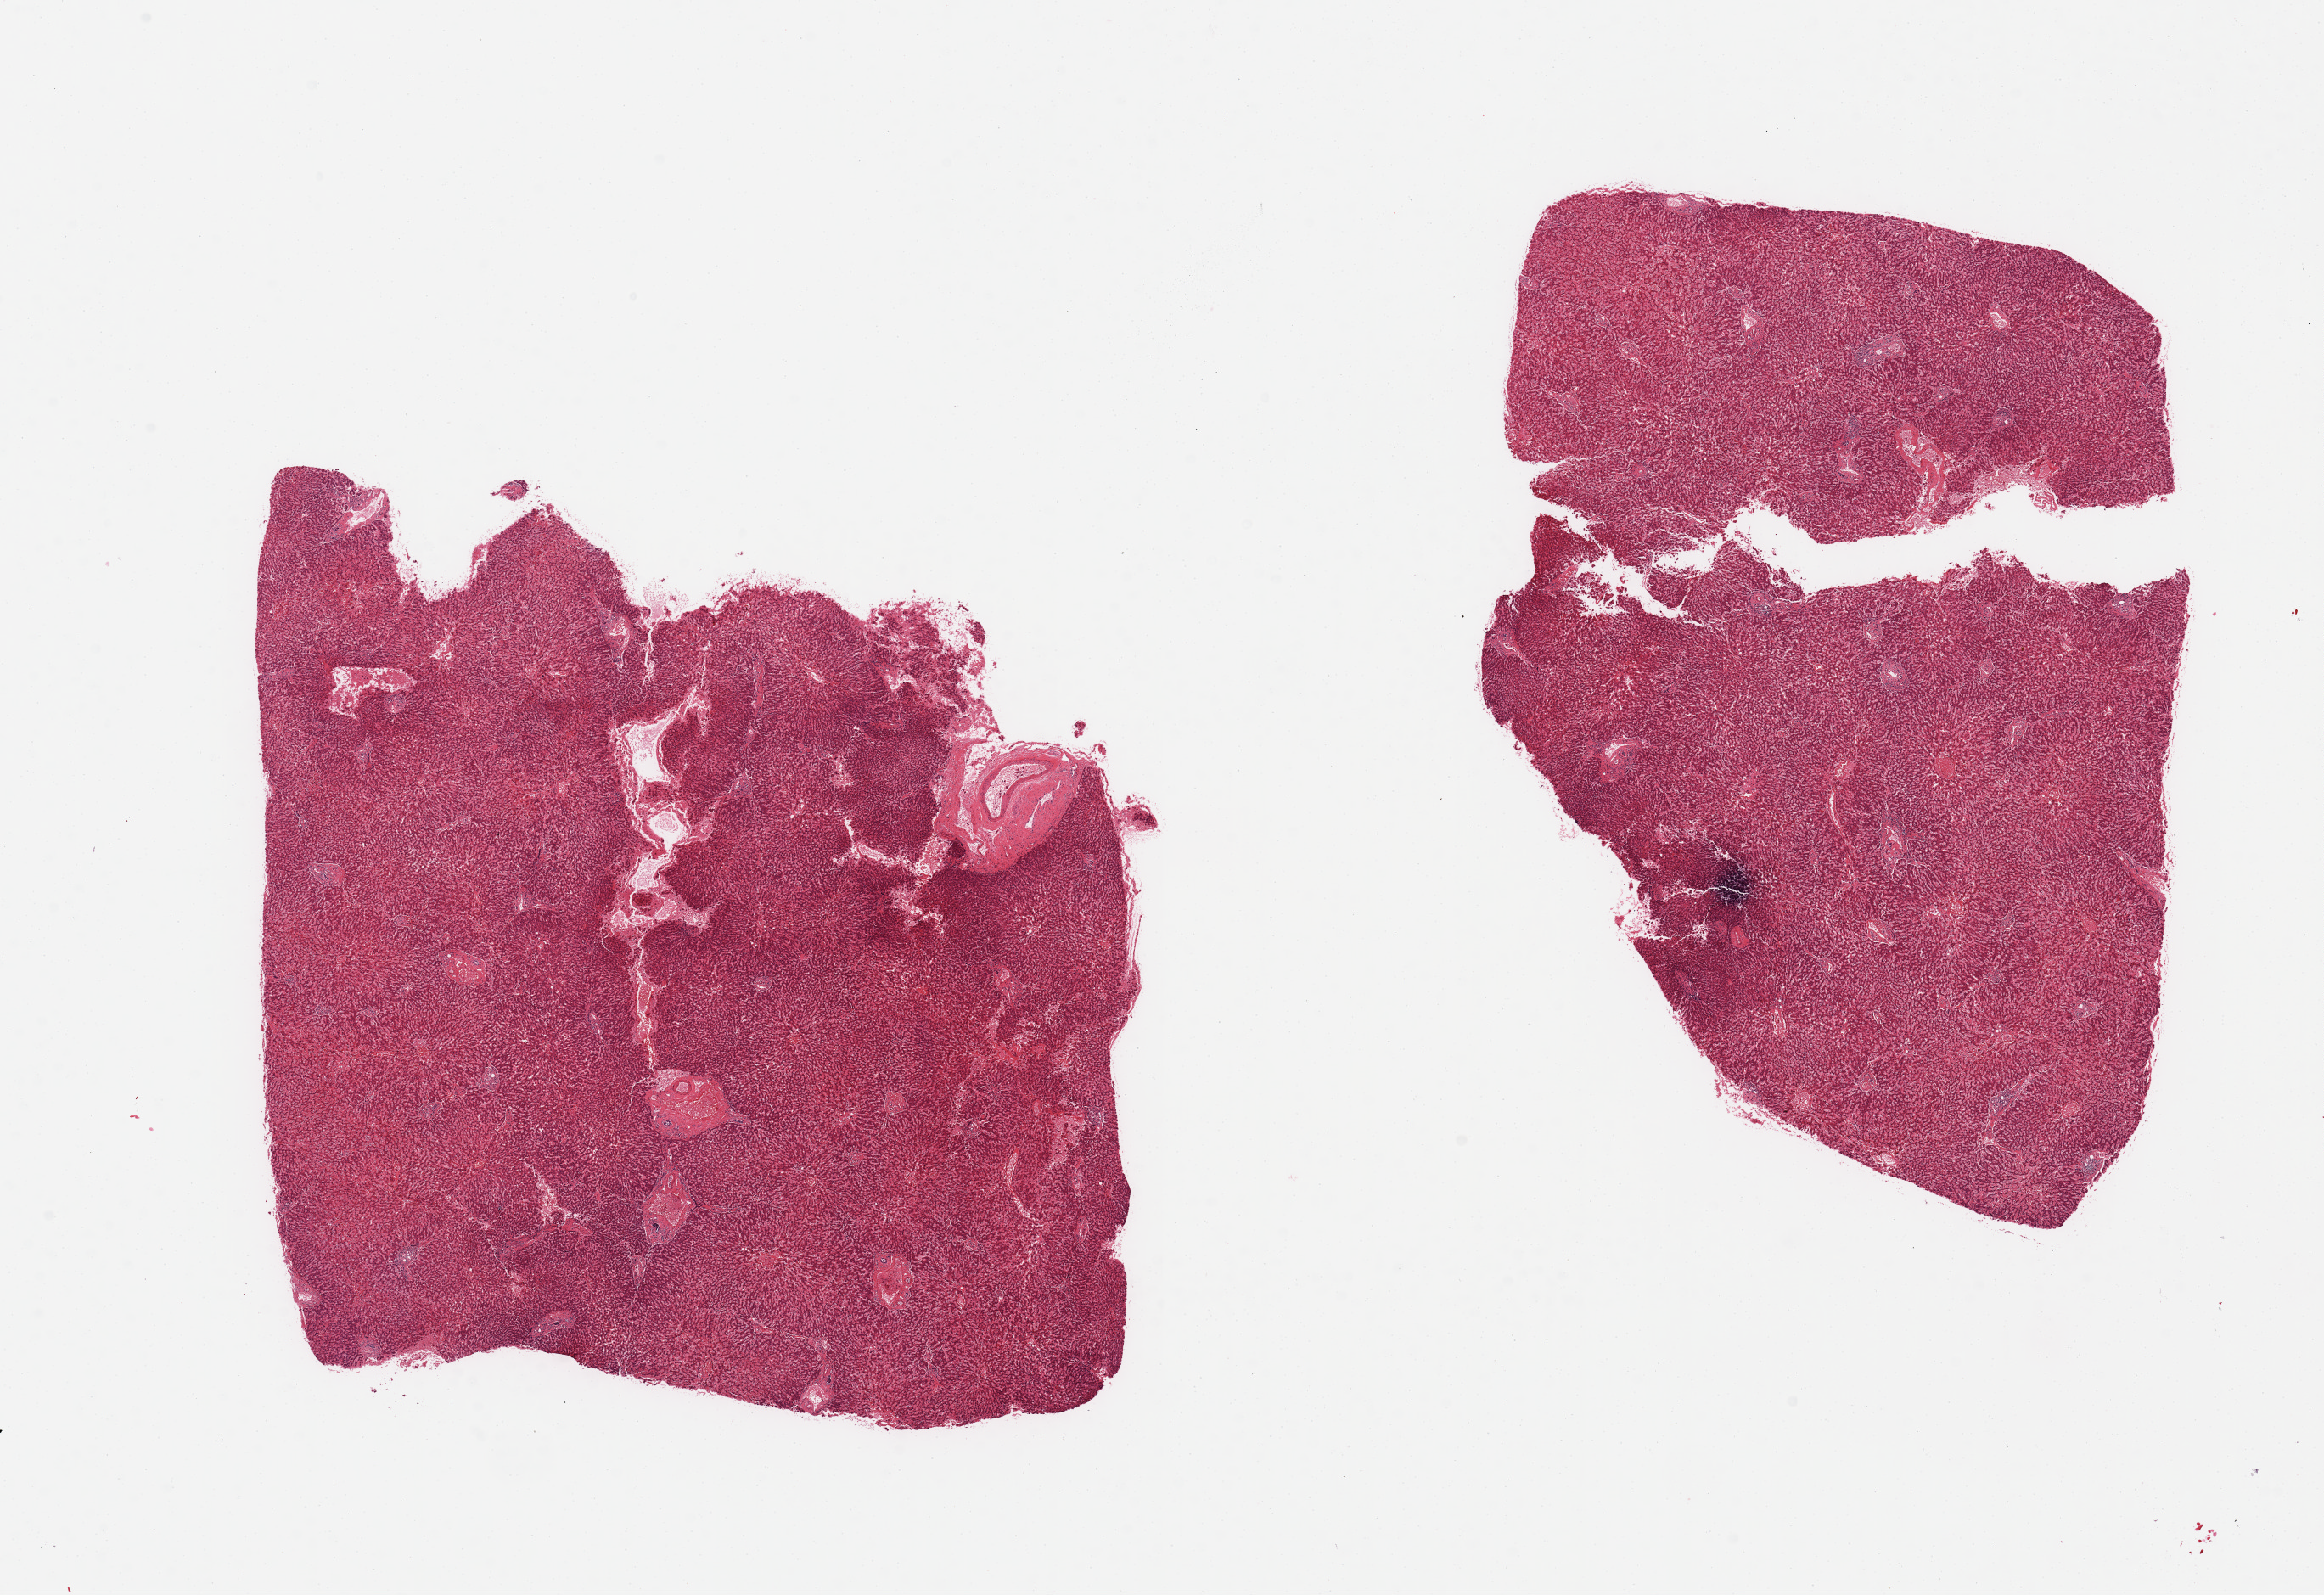
Hematoxylin and eosin (H&E) whole-slide image — low-resolution overview of the scanned area, about 21.7 x 14.9 mm (slide scanned at 20x); PAXgene-fixed, paraffin-embedded tissue; target tissue: liver; donor tissue sample. Donor: female.
• pathologist's review note for this sample: 2 pieces; no fat or significant lesions